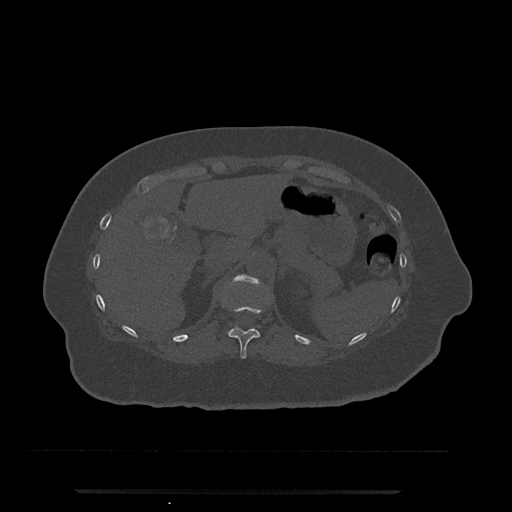
CT including the spine, one axial slice. Position 209 of 797 along the scan axis. Bone window (W 1800 / L 400 HU). 0.5 mm slice thickness. 512 × 512 image matrix, field of view 440 × 440 mm. Patient: female, 51 years. Case-level facts recorded for this patient, not image findings: primary cancer: neuro; vertebrae with lytic lesions (as recorded): T8.
Structures marked on this image (semi-automatically segmented with operator editing):
- T11 vertebra: bounding box (x1, y1, x2, y2) in pixels: (223, 303, 262, 359)
- T12 vertebra: (237, 274, 259, 282)